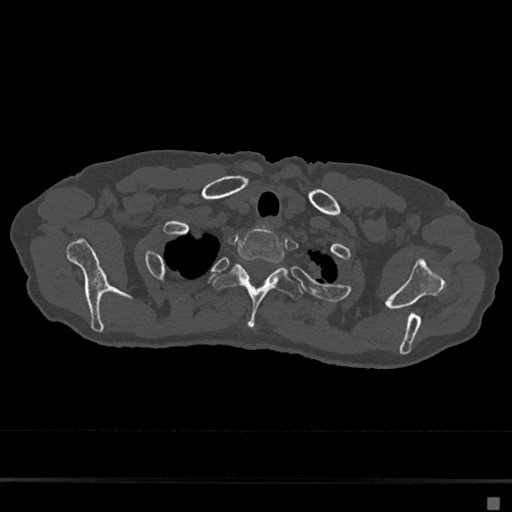
CT including the spine, one axial slice; position 588 of 797 along the scan axis; bone window (W 1800 / L 400 HU); 0.5 mm slice thickness; 512 × 512 image matrix, field of view 360 × 360 mm. Patient: female, 68 years. From the clinical record (not read from this slice): primary cancer: renal.
Structures marked on this image (semi-automatic segmentation, software-assisted and operator-edited):
- T1 vertebra: box from (x=237, y=228) to (x=285, y=263) px
- T2 vertebra: (x=212, y=263)–(x=303, y=329)